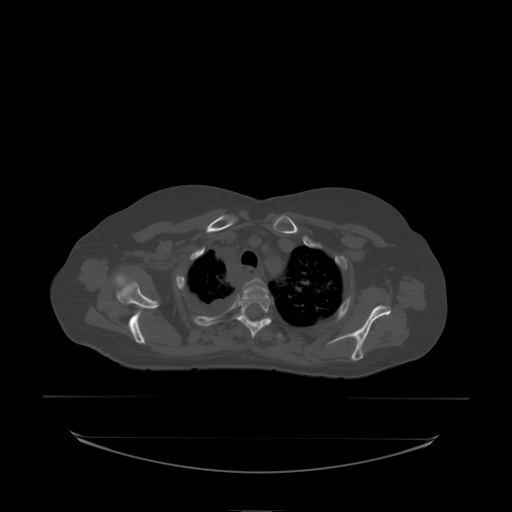
CT including the spine, one axial slice. Slice 174 of 242 in the series (ordered by position). Bone window (W 1800 / L 400 HU). 2.5 mm slice thickness. 512 × 512 image matrix, field of view 500 × 500 mm. Patient: female, 53 years. Case-level facts recorded for this patient, not image findings: primary cancer: lung.
Structures marked on this image (semi-automatically segmented with operator editing):
- T2 vertebra: bounding box <241,279,269,300> (left, top, right, bottom; pixels)
- T3 vertebra: <234,292,272,338>
- T4 vertebra: <239,316,269,325>